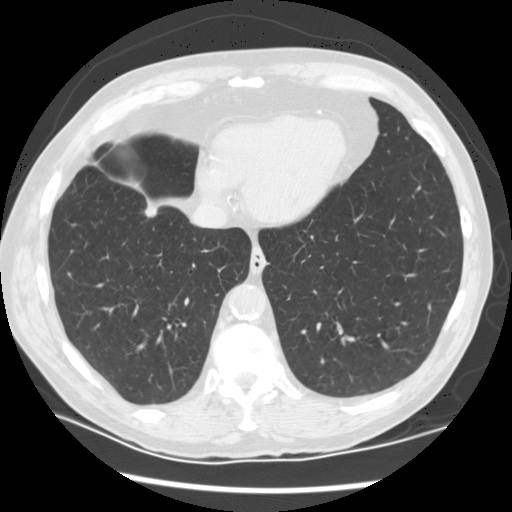
Chest CT (low-dose screening protocol), one axial image; first (baseline) screen; lung window (W 1500 / L -600 HU); standard (soft-tissue) reconstruction kernel (STANDARD); slice 94 of 122 in the series. Male participant, aged 68 years at enrolment. Current smoker at enrolment.
• Expert-annotated lung lesion, bounding box (x1, y1, x2, y2) in pixels: (121, 190, 180, 236).
• The screening reader recorded 3 non-calcified nodules or masses ≥4 mm on this exam; which of them this box marks is not recorded.
• Later outcome: lung cancer diagnosed 90 days after this screen — adenocarcinoma, NOS, right upper lobe, right lower lobe, well differentiated (G1), stage IV (AJCC 6th edition), 35 mm at pathology.